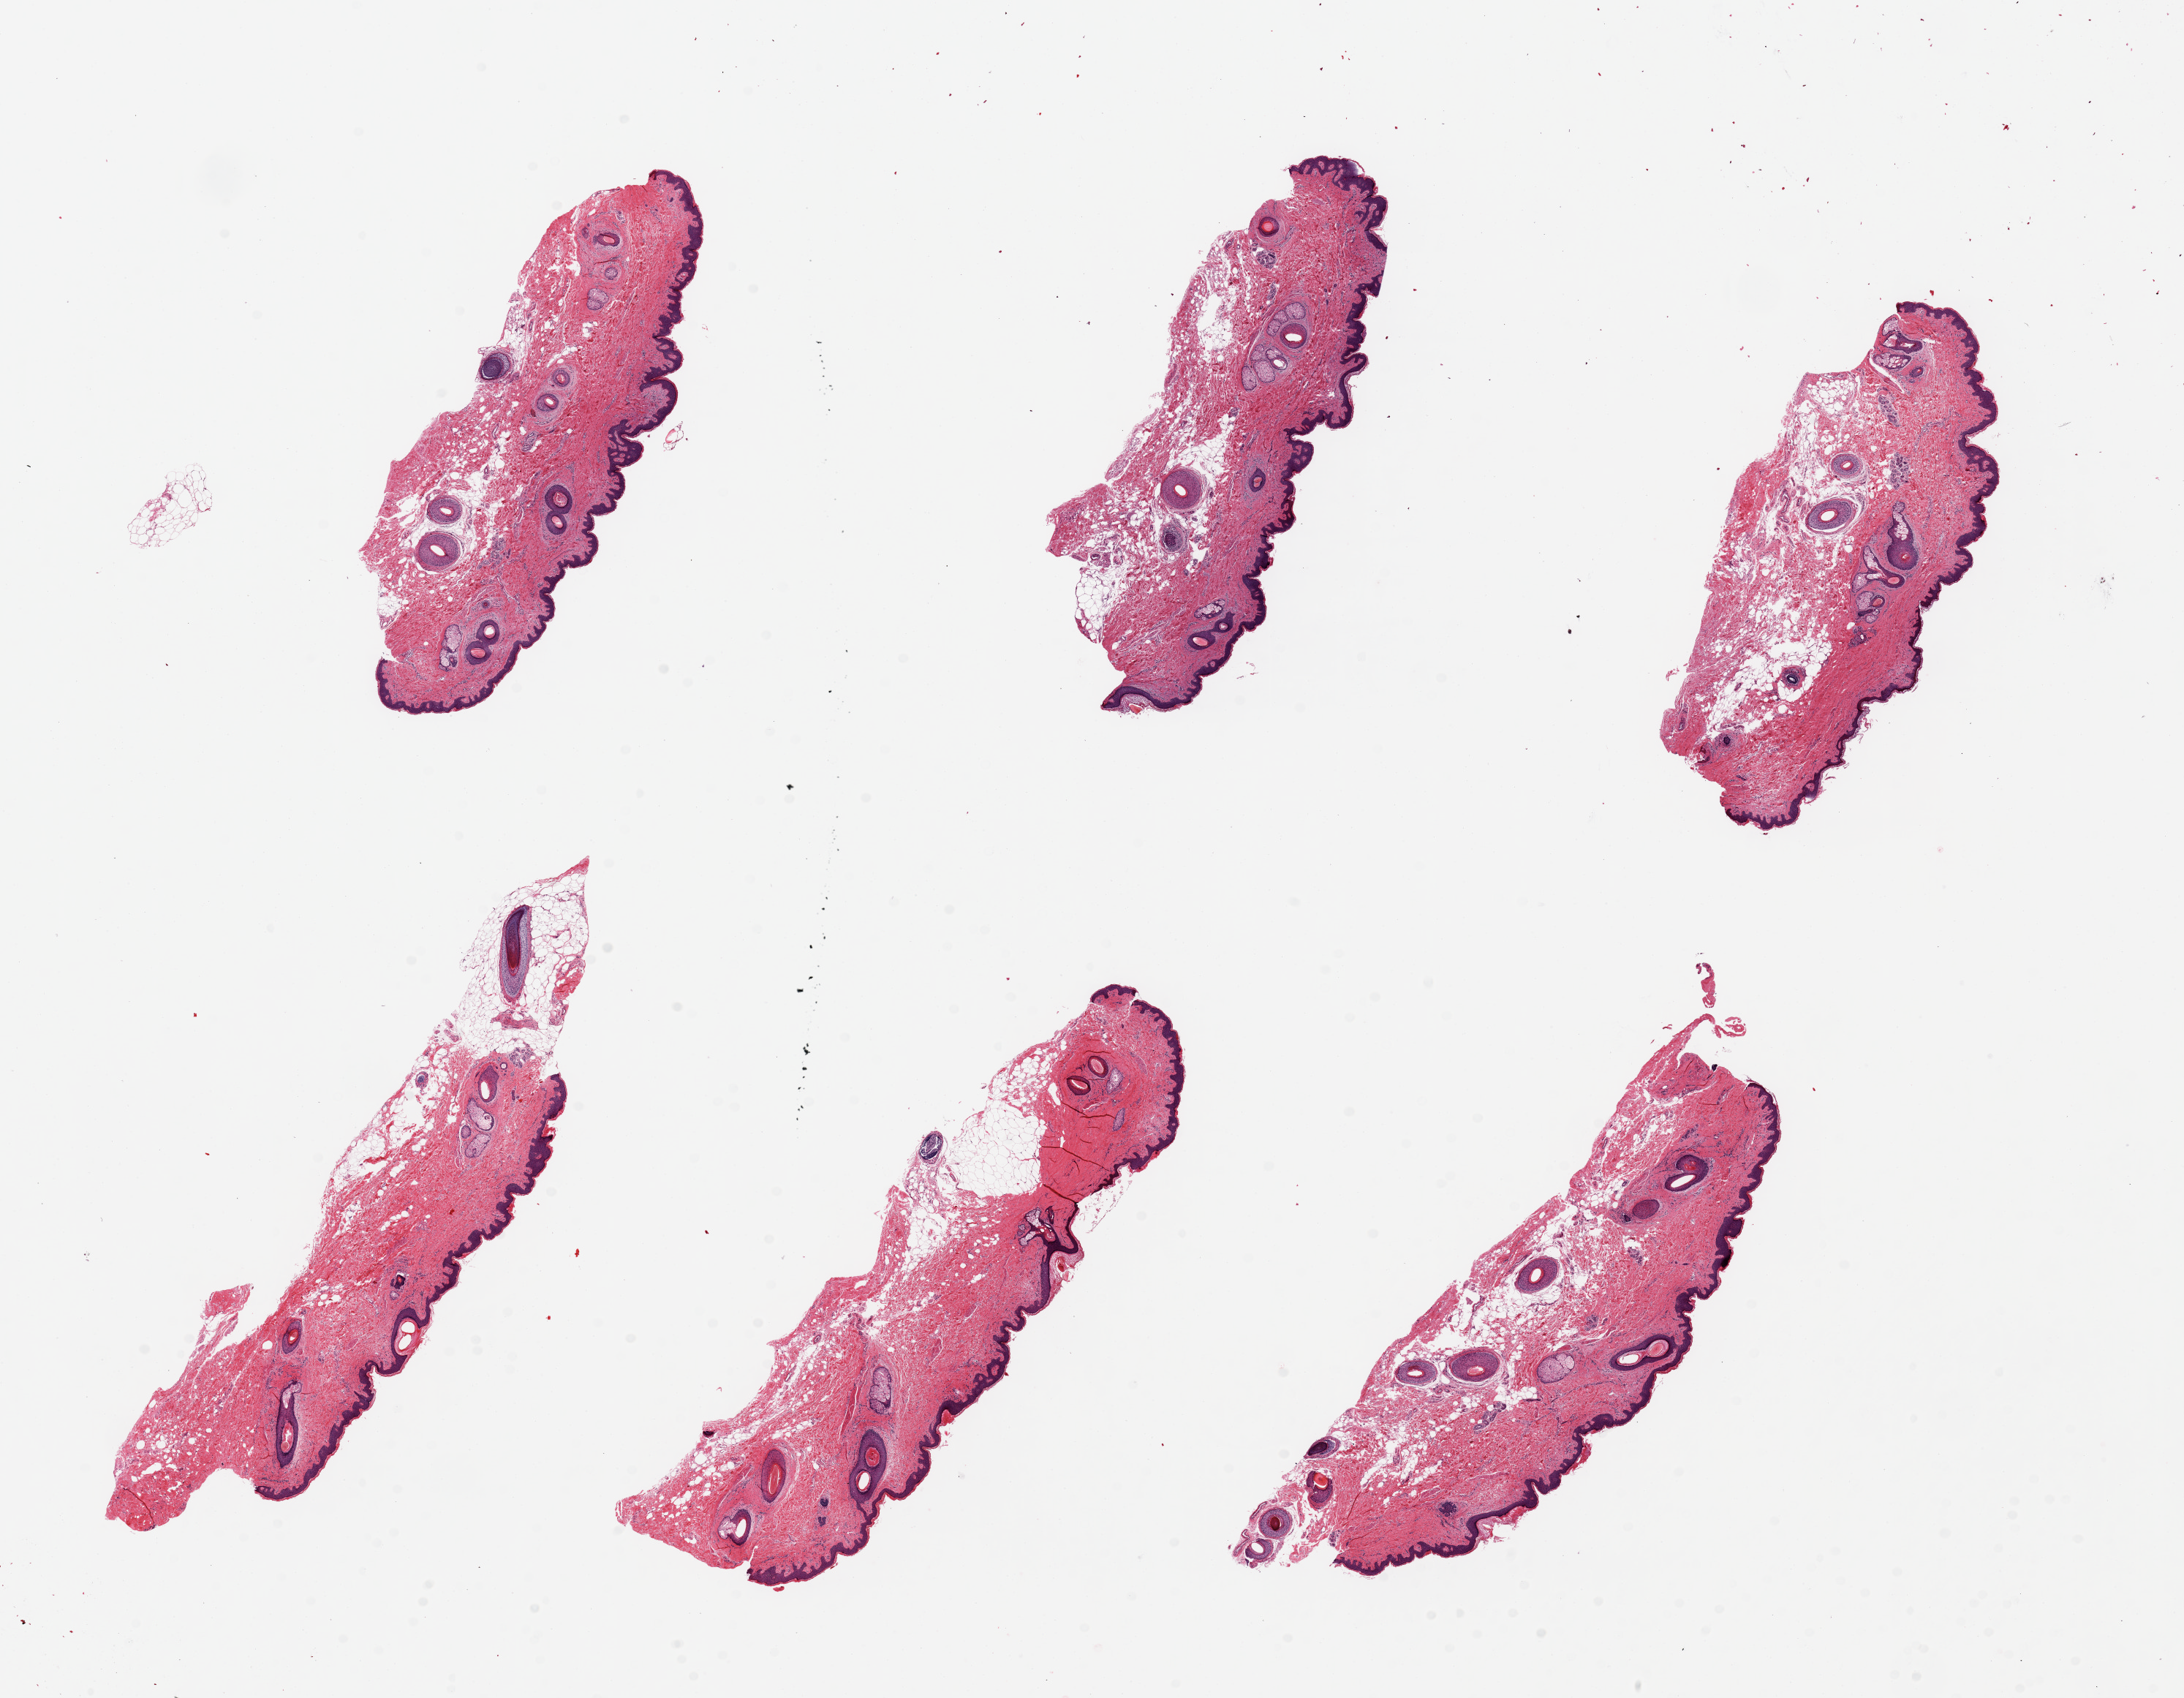
Digitized haematoxylin and eosin-stained section — a low-resolution overview of the entire scanned area, about 23.6 x 18.4 mm; PAXgene-fixed paraffin-embedded (PFPE) section; target tissue: skin of suprapubic region; tissue donor sample. Donor sex: female.
• pathologist's review note for this sample: 6 pieces ~6x2mm